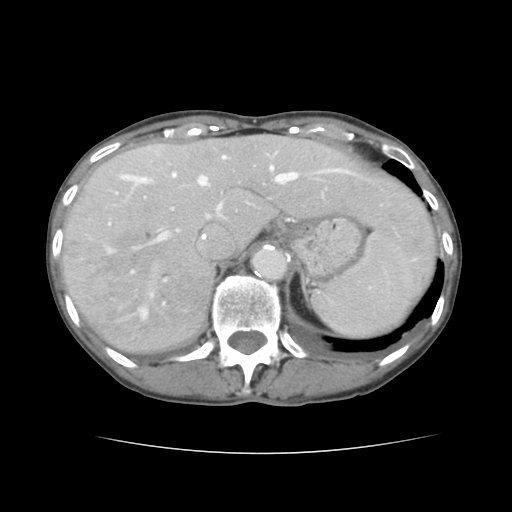
Contrast-enhanced abdominal CT, one axial slice. Position 106 of 136 along the scan axis. Intravenous contrast given. Soft-tissue window (W 400 / L 40 HU). 512 × 512 image matrix, field of view 319 × 319 mm. Female patient, age 77 years. From the clinical record (not read from this slice): diagnosis: colorectal cancer liver metastases, imaged before liver resection.
Outlined on this slice (outlined manually by an expert reader):
- hepatic veins: bounding box [x1, y1, x2, y2] px = [112, 156, 345, 317]
- liver: [63, 136, 436, 355]
- planned liver remnant (the part of the liver to remain after resection): [162, 136, 435, 270]
- portal vein (with intrahepatic branches): [109, 153, 384, 304]